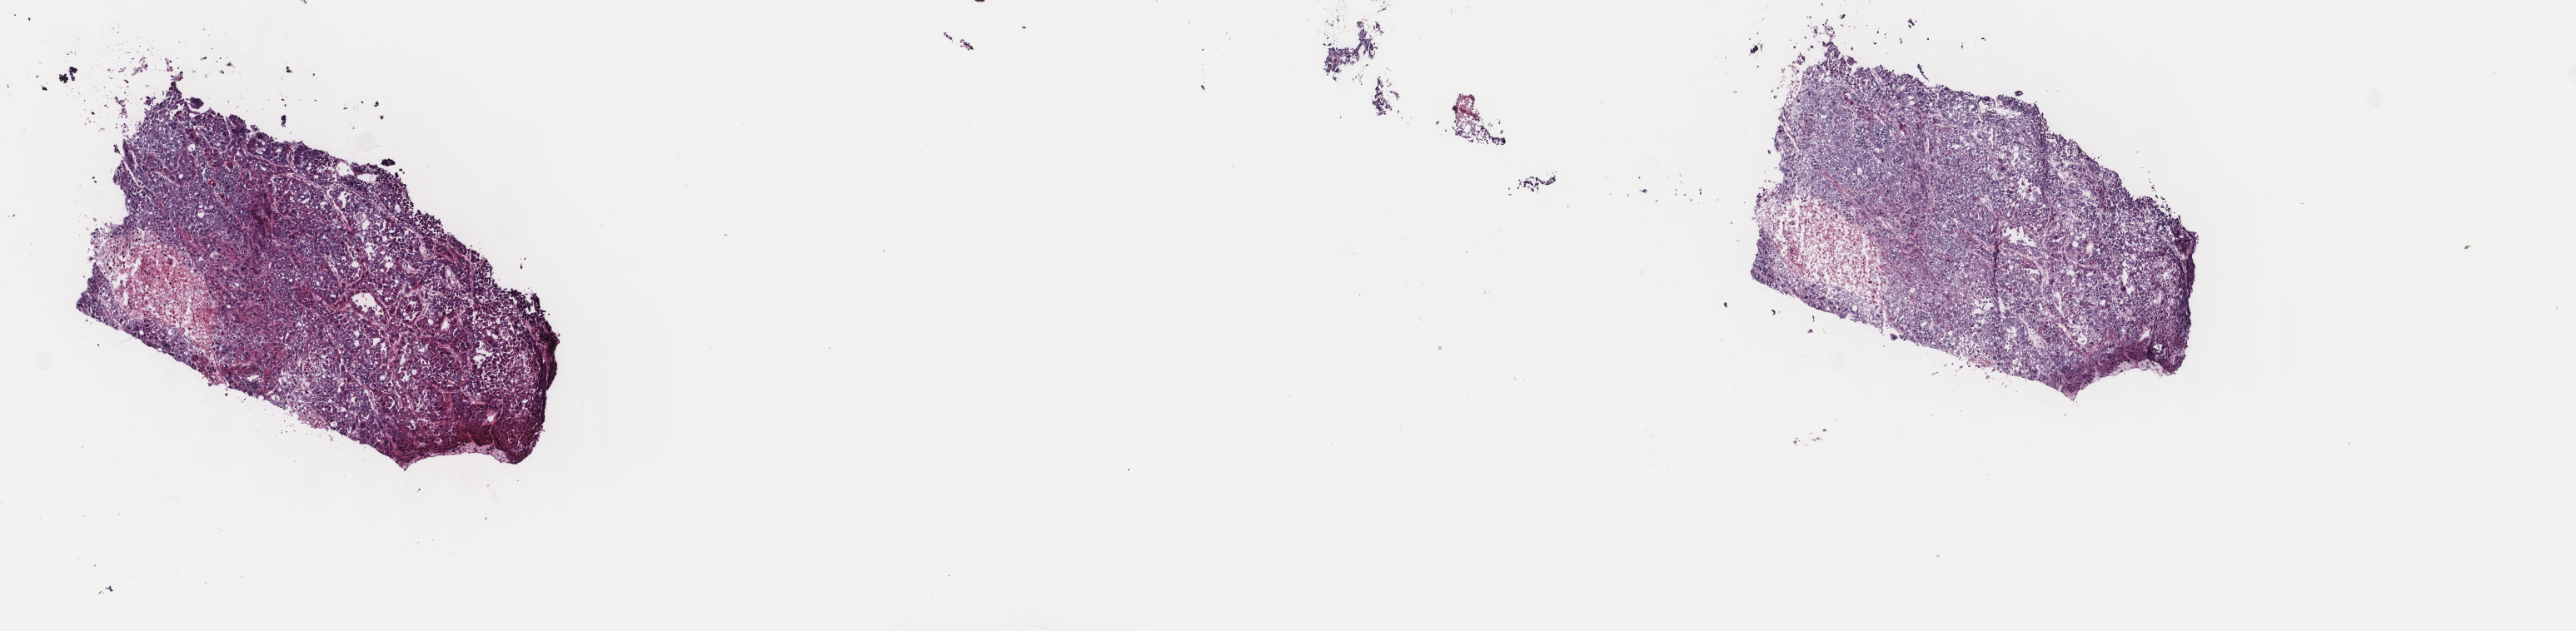
Whole-slide histology image, H&E-stained — whole scanned area (about 12.3 x 3.0 mm) shown as a low-resolution overview; frozen section; lung, primary tumour sample. Female, age 65 years at initial diagnosis. Composition of this section per pathologist review: tumour cells 87%, tumour nuclei 93%, normal cells 0%, stromal cells 0%, necrosis 13%. Infiltration values recorded for this section: lymphocyte infiltration 0%, monocyte infiltration 0%, neutrophil infiltration 0%.
• AJCC pathologic stage: IB
• pathologic diagnosis: Adenocarcinoma, NOS (lower lobe, lung)